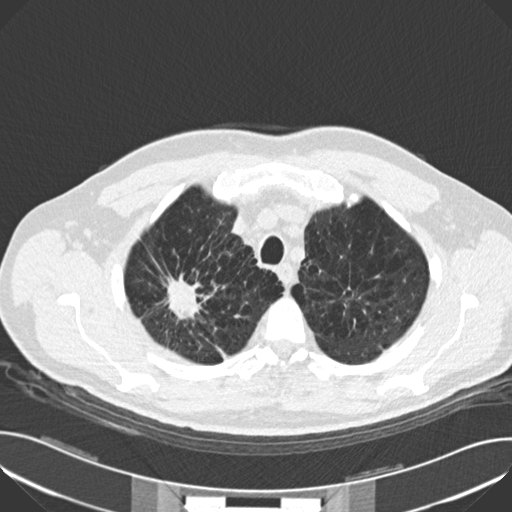
Low-dose screening chest CT, one axial slice. Position 135 of 159 along the scan axis. Reconstruction kernel B30f. 120 kVp. Lung window (W 1500 / L -600 HU). 2 mm slice thickness. 512 × 512 image matrix, field of view 380 × 380 mm.
Structures marked on this image (outlined manually by an expert reader):
- lesion 1 (tumor, upper lobe of right lung): bounding box (x1, y1, x2, y2) in pixels: (166, 276, 200, 319)